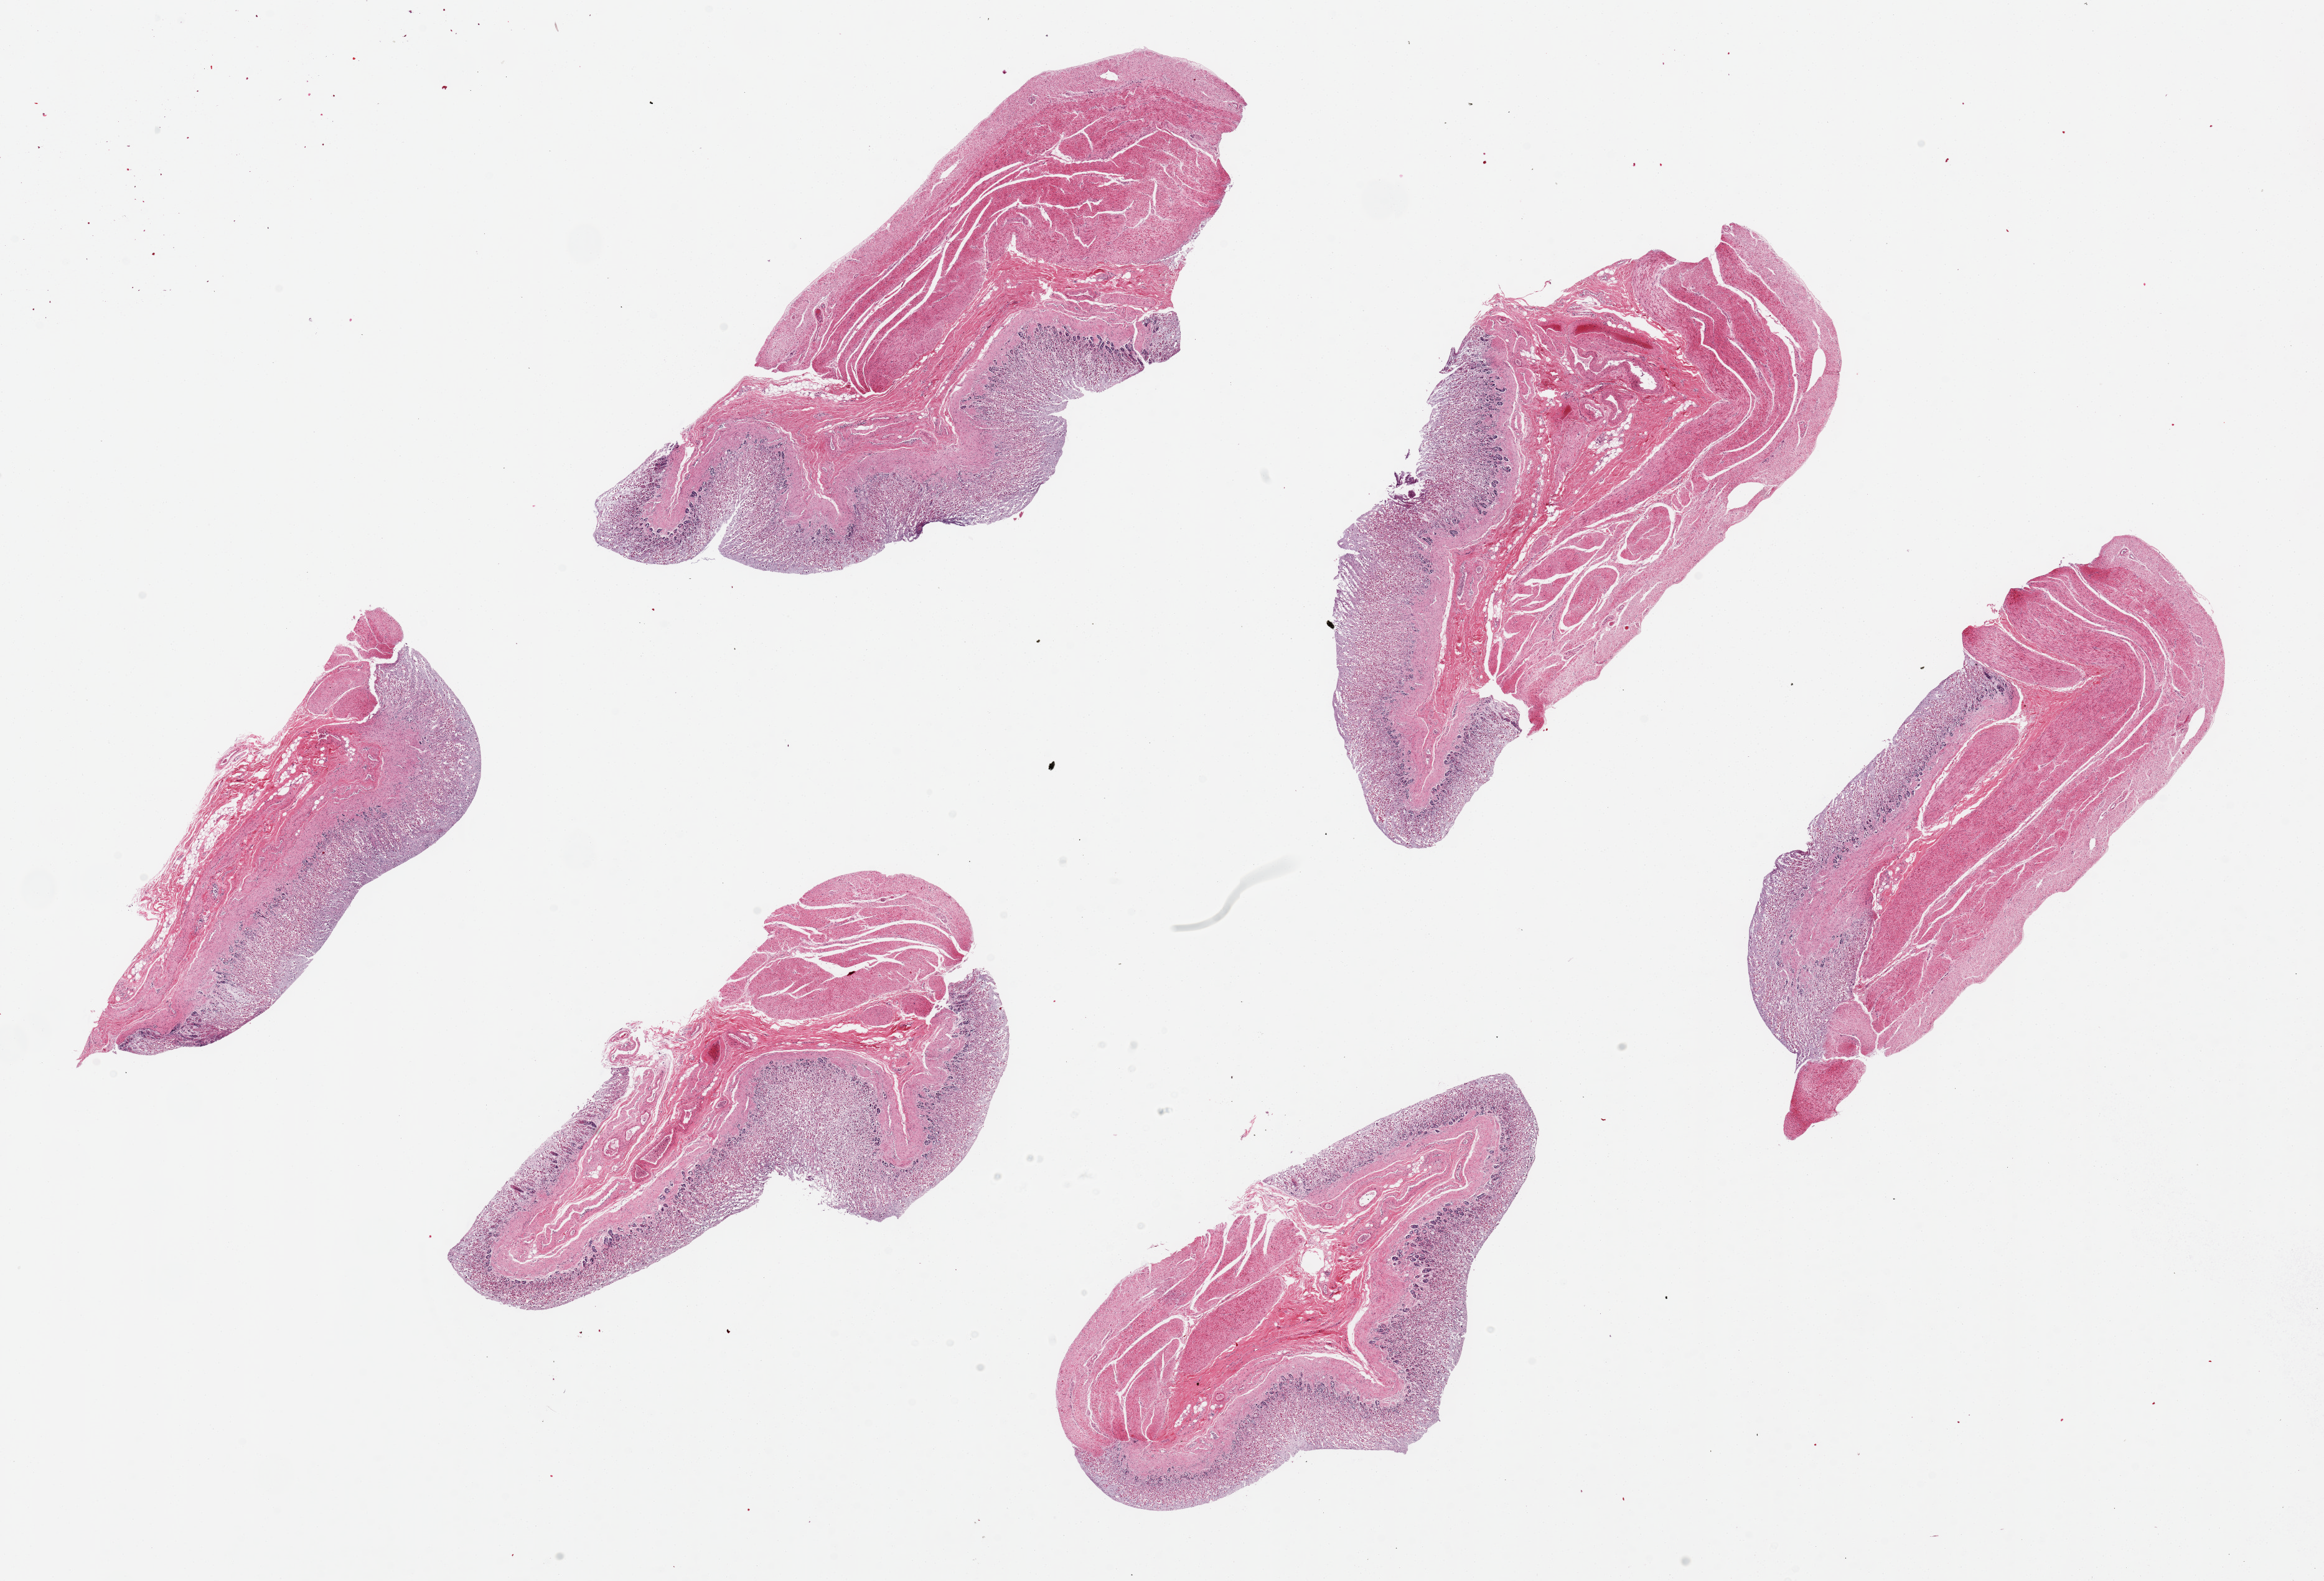
Digitized hematoxylin and eosin (H&E)-stained section, brightfield — a low-resolution overview of the entire scanned area, about 29.5 x 20.1 mm (slide scanned at 20x). PAXgene-fixed paraffin-embedded (PFPE) section. Section of stomach (target tissue). Donor tissue sample. Female donor.
Pathologist's review note for this sample: 6 pieces up to 9x4 mm; mucosa largely autolyzed; muscularis slight autolysis.